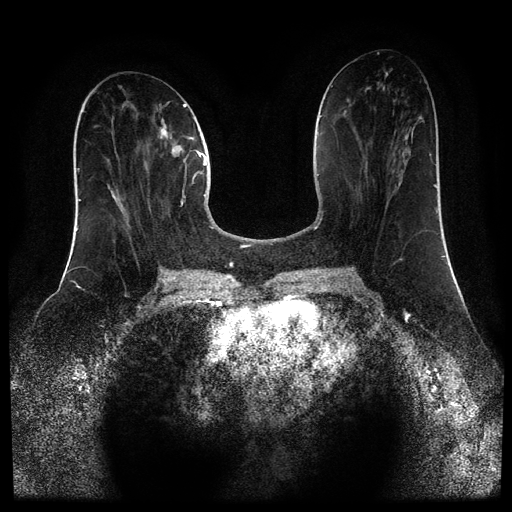
Breast MRI (dynamic contrast-enhanced, multi-phase), one axial slice; dynamic contrast-enhanced series, time point 2 of 5 at this slice position (early post-contrast); 1.5 T; TE 2.6 ms, TR 5.4 ms; 2 mm slice thickness; 512 × 512 image matrix, field of view 340 × 340 mm. Patient: female, 43 years.
Annotated regions visible in this slice (semi-automatic segmentation, software-assisted and operator-edited):
- breast lesion (labelled 'tumour' in the annotation; benign lesions carry a separate 'benign' label): bounding box (x1, y1, x2, y2) in pixels: (158, 119, 183, 157)